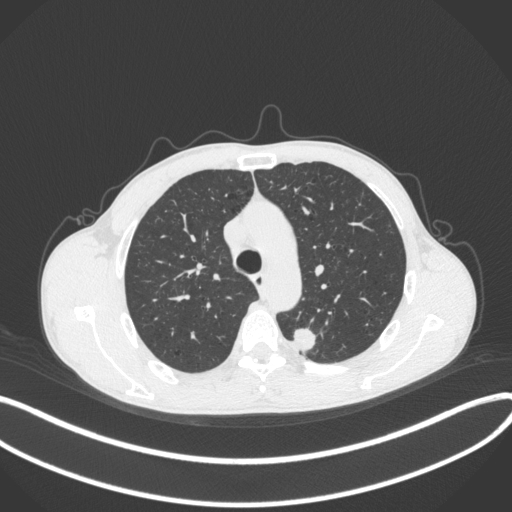
Chest CT, one axial slice. Position 290 of 429 along the scan axis. 120 kVp. Lung window (W 1500 / L -600 HU). 1 mm slice thickness. 512 × 512 image matrix. Male patient, age 51 years. Case-level facts recorded for this patient, not image findings: clinical TNM (as recorded): T2a N1 M1.
Annotated regions visible in this slice (bounding box drawn by a radiologist):
- lung tumour (recorded histology: adenocarcinoma): bounding box <293,325,317,353> (left, top, right, bottom; pixels)